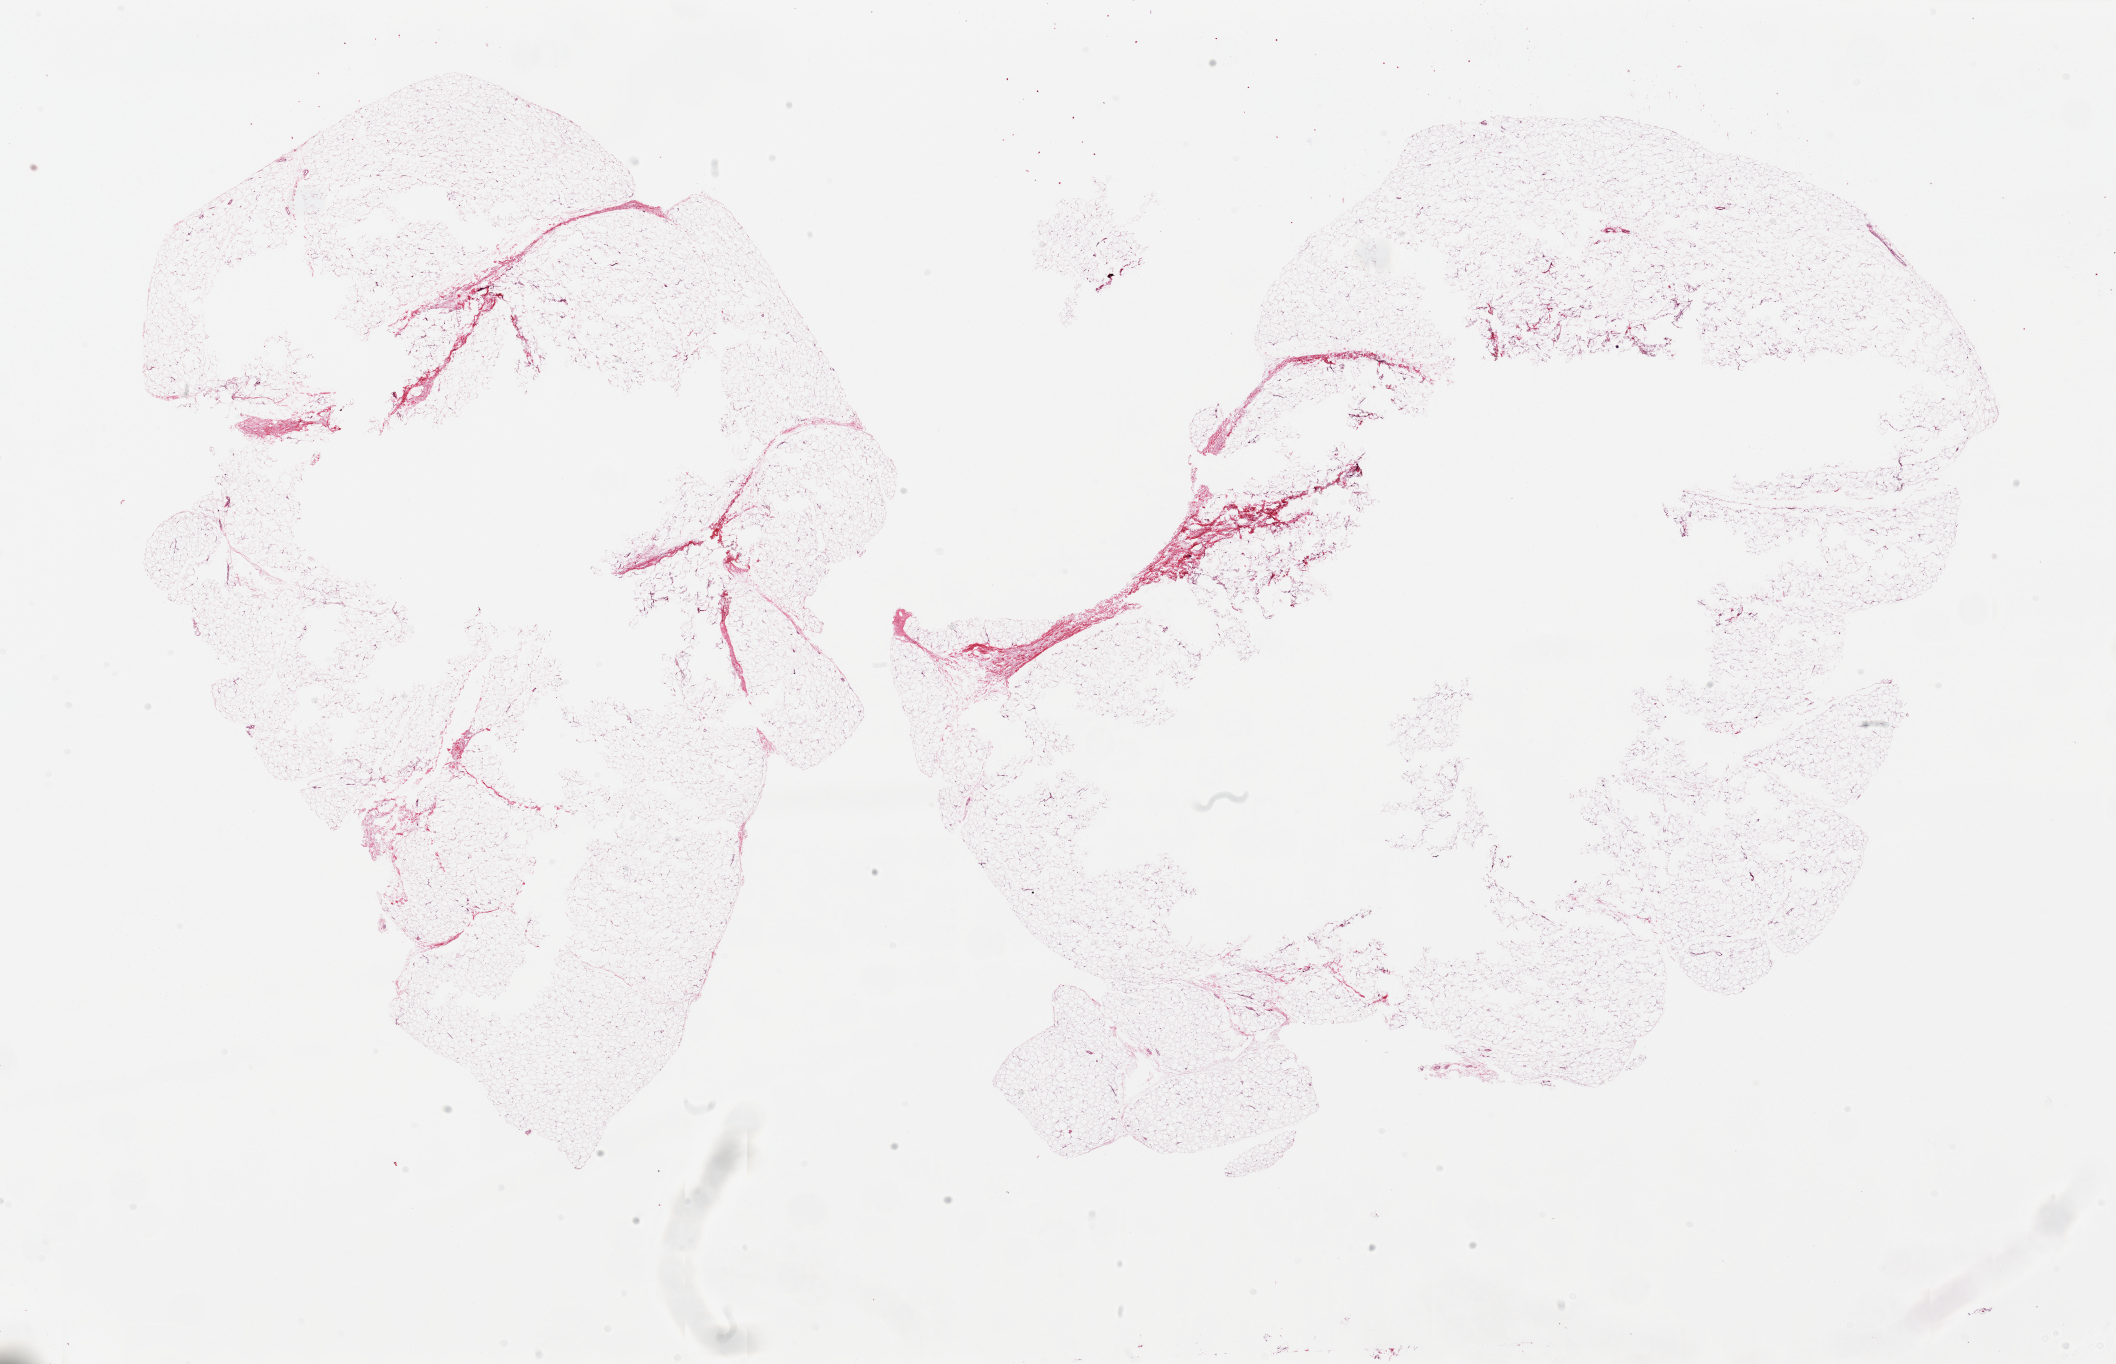
Haematoxylin and eosin whole-slide image — whole scanned area (about 33.5 x 21.6 mm, slide scanned at 20x) shown as a low-resolution overview, PAXgene-fixed, paraffin-embedded tissue, sampled site (target tissue): adipose tissue, tissue donor sample. Female donor.
* reviewer comment on this tissue sample: 2 pieces, large aliquots 17x11 mm,15x15 mm; central, probably unfixed, defects